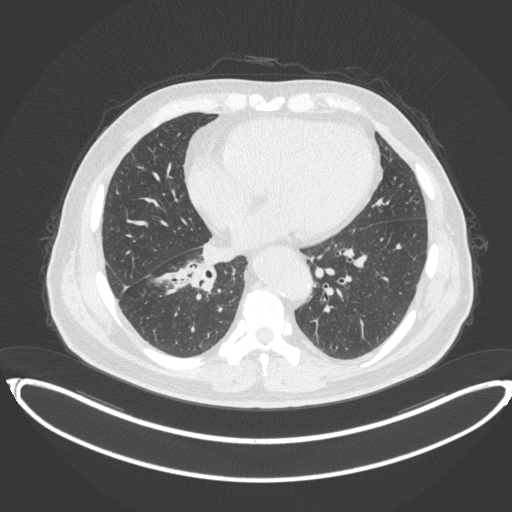
Chest CT, one axial slice. Slice 161 of 383 in the series (ordered by position). Reconstruction kernel B31f. 120 kVp. Lung window (W 1500 / L -600 HU). 1 mm slice thickness. 512 × 512 image matrix. Patient: male, 61 years. From the clinical record (not read from this slice): clinical TNM (as recorded): T1b N1 M0.
Outlined on this slice (rectangle marked by the reading radiologist):
- lung tumour (recorded histology: squamous cell carcinoma): bounding box <179,255,220,293> (left, top, right, bottom; pixels)